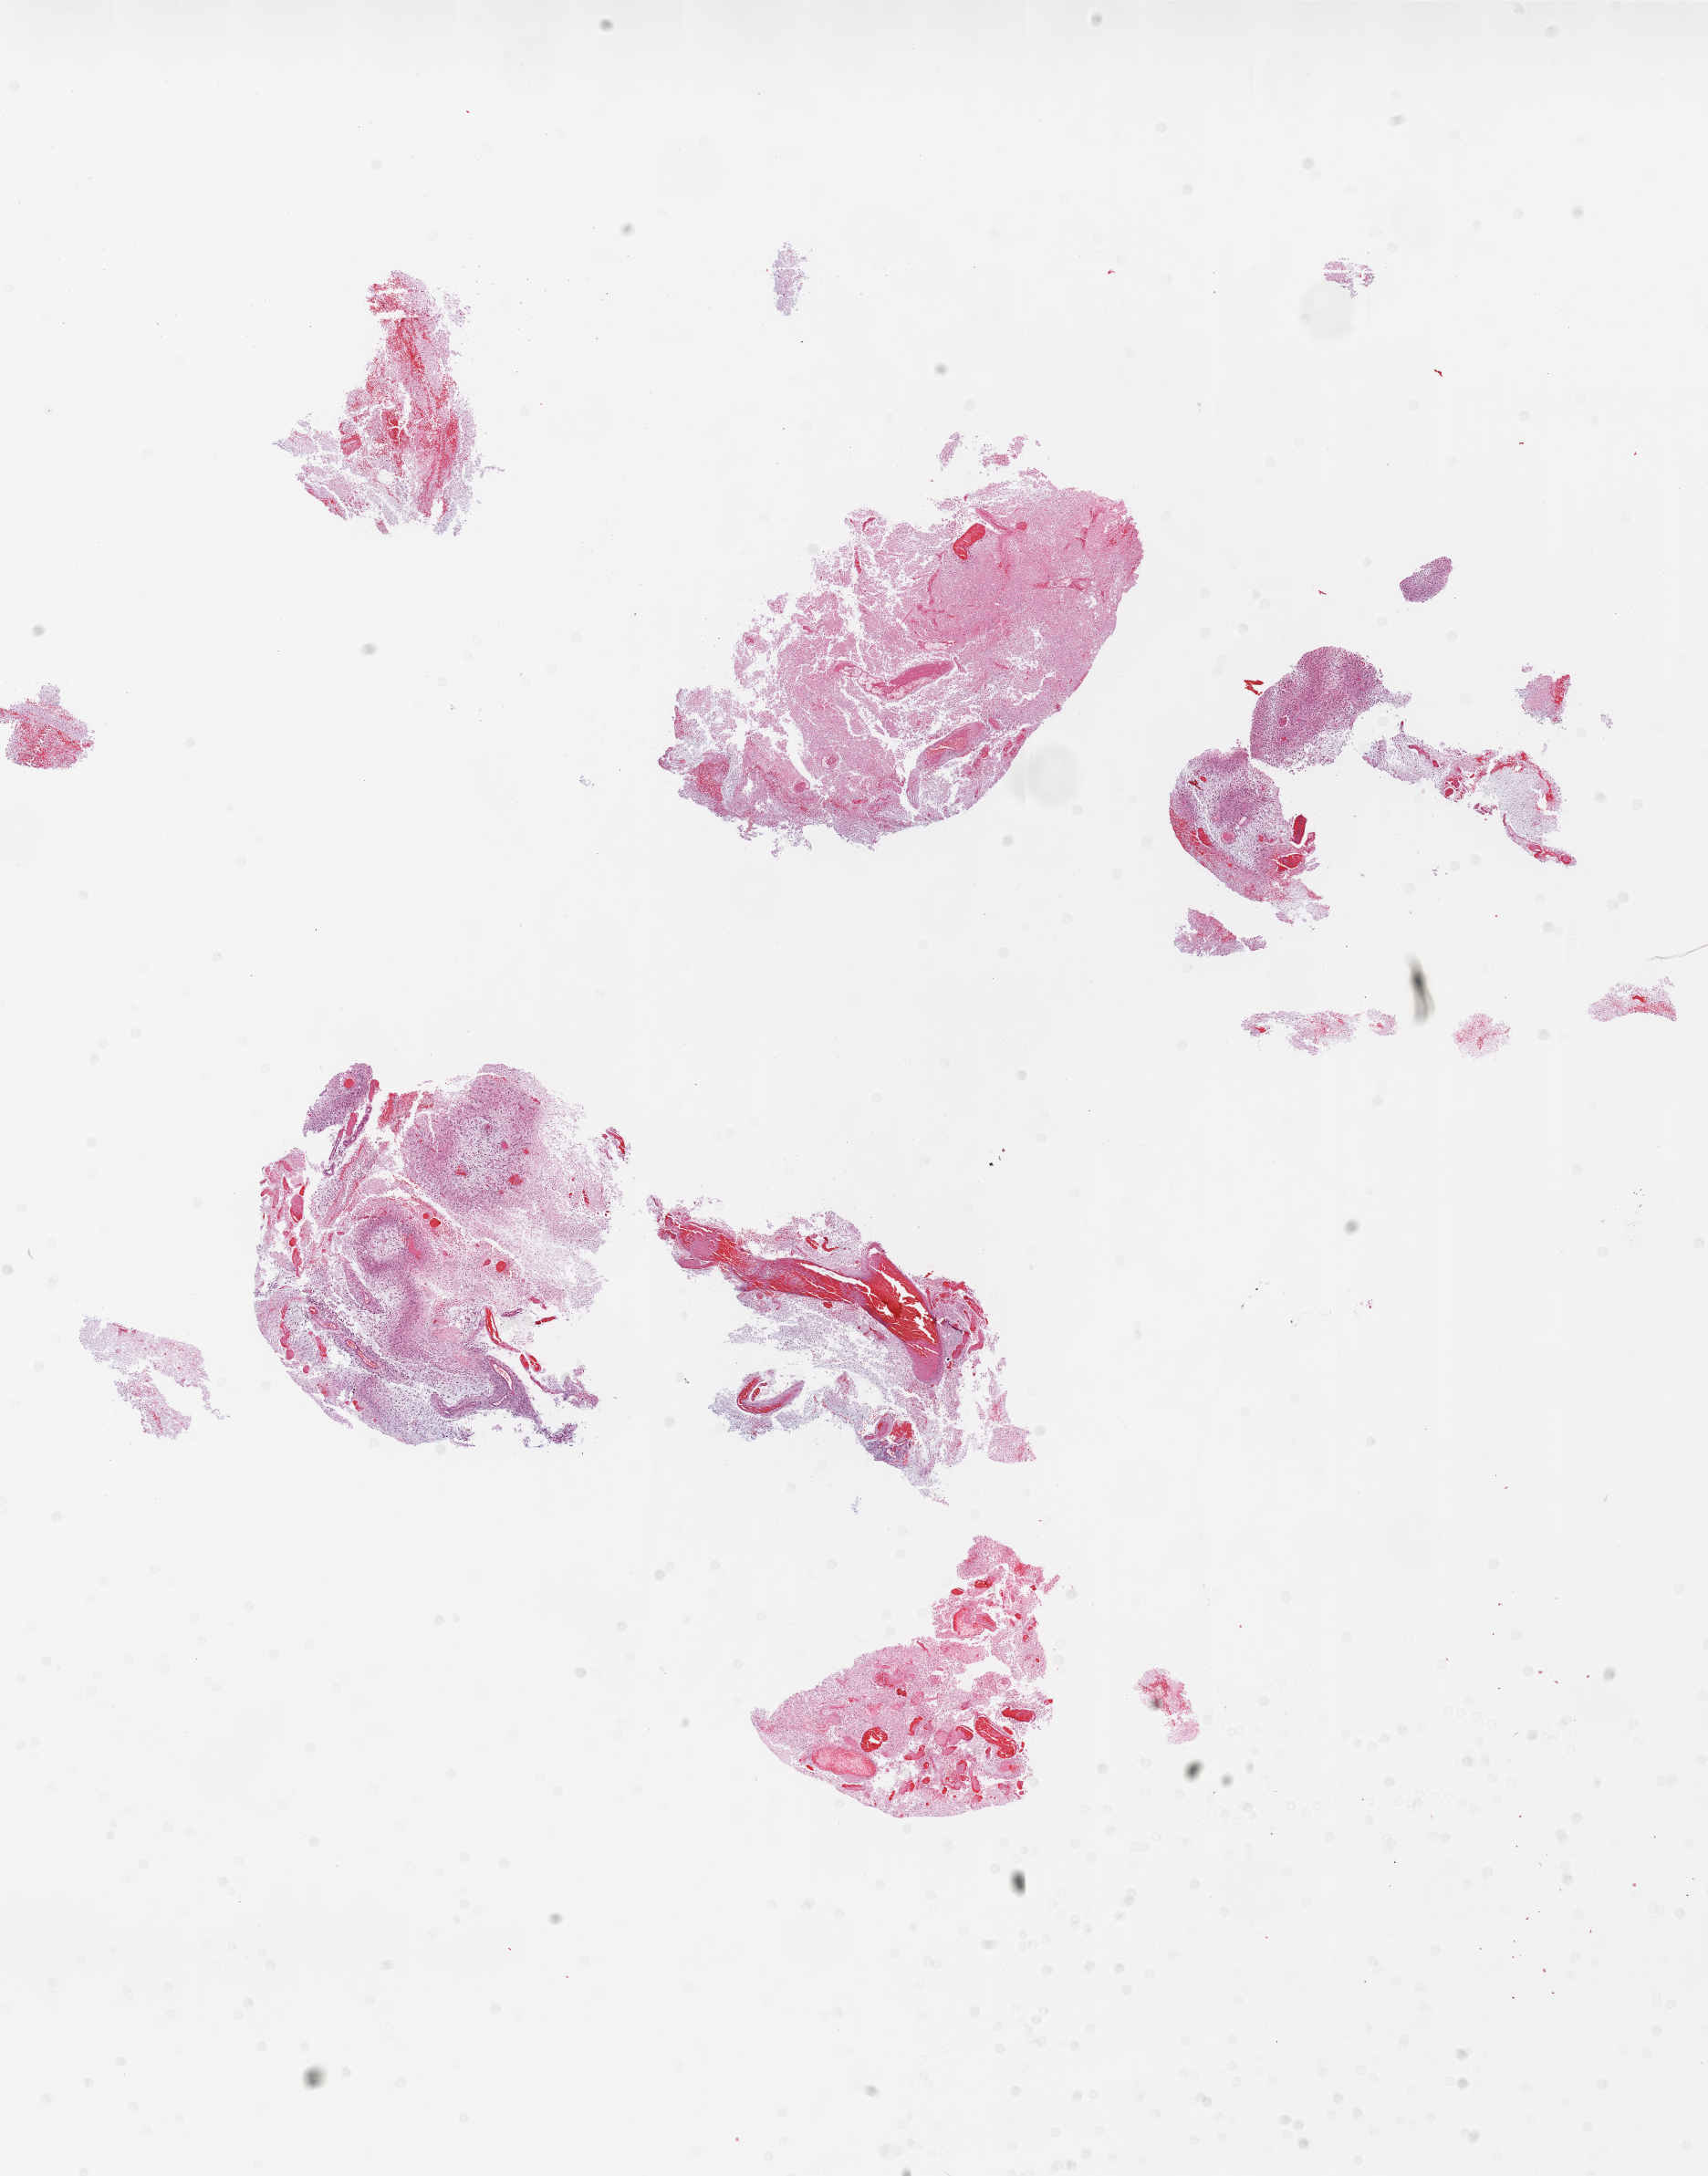
Digitized Hematoxylin and eosin (H&E) stained tissue section (whole slide), whole scanned area (about 15.0 x 19.1 mm, from a 20x scan) shown as a low-resolution overview, formalin-fixed paraffin-embedded (FFPE) diagnostic section, sample: primary tumour, brain. Female patient; age at initial diagnosis 51 years.
Pathologic diagnosis: Glioblastoma.